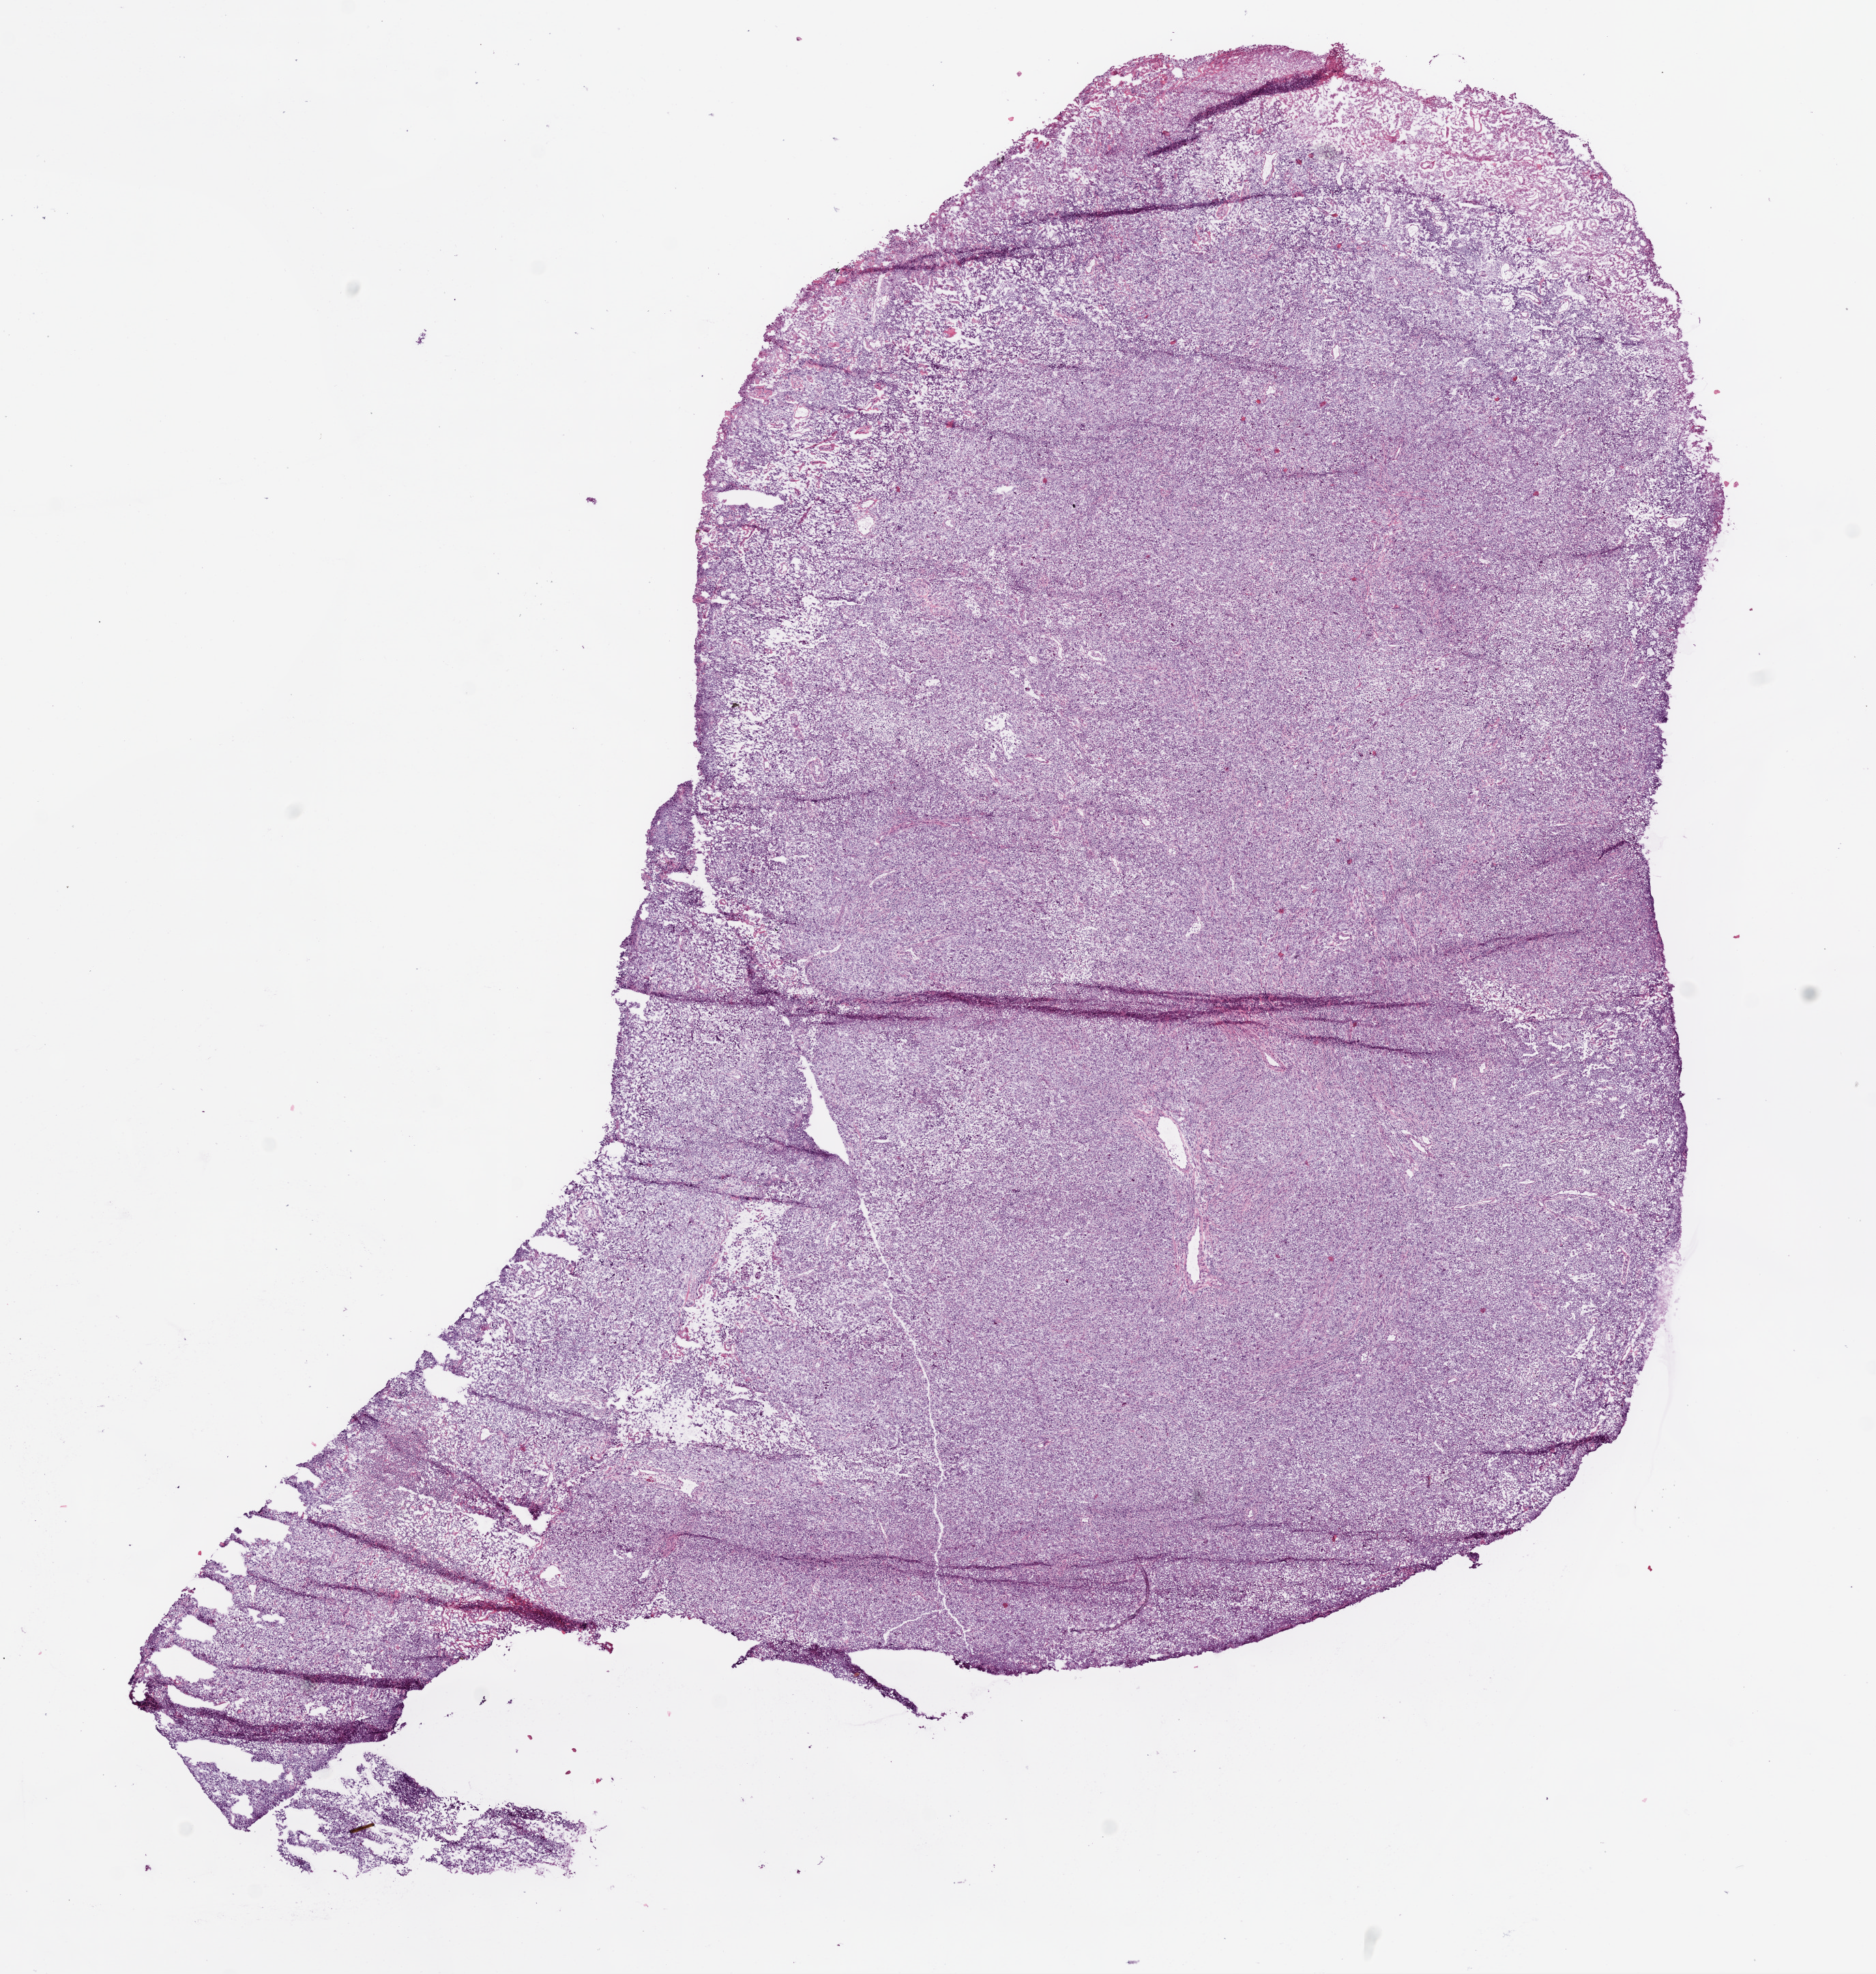
H&E whole-slide image — a low-resolution overview of the entire scanned area, about 11.0 x 11.6 mm (from a 20x scan). Frozen section. Sample: primary tumour, lung. Male patient; age at initial diagnosis 69 years.
Diagnosis: Squamous cell carcinoma, NOS (upper lobe, lung).